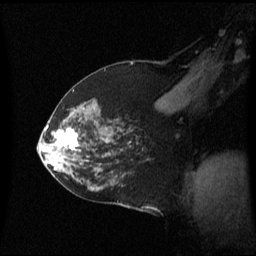
Breast MRI (dynamic contrast-enhanced), one sagittal slice. Dynamic contrast-enhanced series, image 2 of 3 at this slice position (ordered by acquisition). 1.5 T. TE 4.2 ms, TR 8.4 ms. 256 × 256 image matrix. Female patient, age 59 years. Case-level facts recorded for this patient, not image findings: setting: breast cancer imaged before/during neoadjuvant chemotherapy; receptor status: HR-positive, HER2-negative.
Outlined on this slice (semi-automatic segmentation, software-assisted and operator-edited):
- analysis volume of interest (the breast-tissue region the enhancement analysis was run in; not a lesion): bounding box [x1, y1, x2, y2] px = [46, 114, 89, 163]
- tumour enhancement mask (voxels above the 70 % enhancement threshold inside the analysis volume of interest): [55, 128, 78, 149]